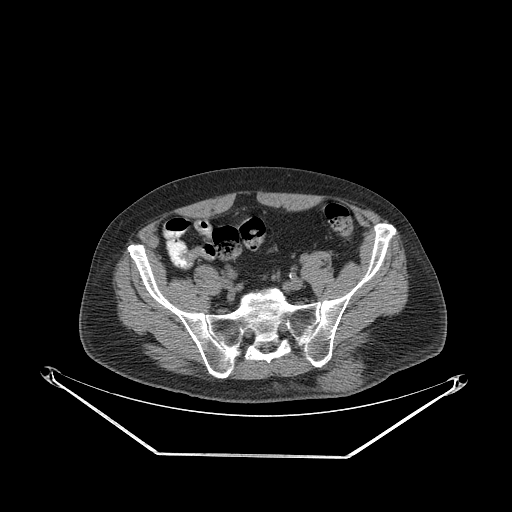
CT of an extremity soft-tissue mass (from a PET/CT study), one axial slice; position 76 of 267 along the scan axis; reconstruction kernel STANDARD; 140 kVp; soft-tissue window (W 400 / L 40 HU); 3.75 mm slice thickness; 512 × 512 image matrix, field of view 500 × 500 mm. Male patient. Case-level facts recorded for this patient, not image findings: histological type: leiomyosarcoma; grade: intermediate; site of the primary tumour: left pelvis.
Structures marked on this image (expert contour drawn on MRI and transferred to this co-registered scan by the dataset authors):
- gross tumour volume (mass): bounding box <324,358,364,394> (left, top, right, bottom; pixels)